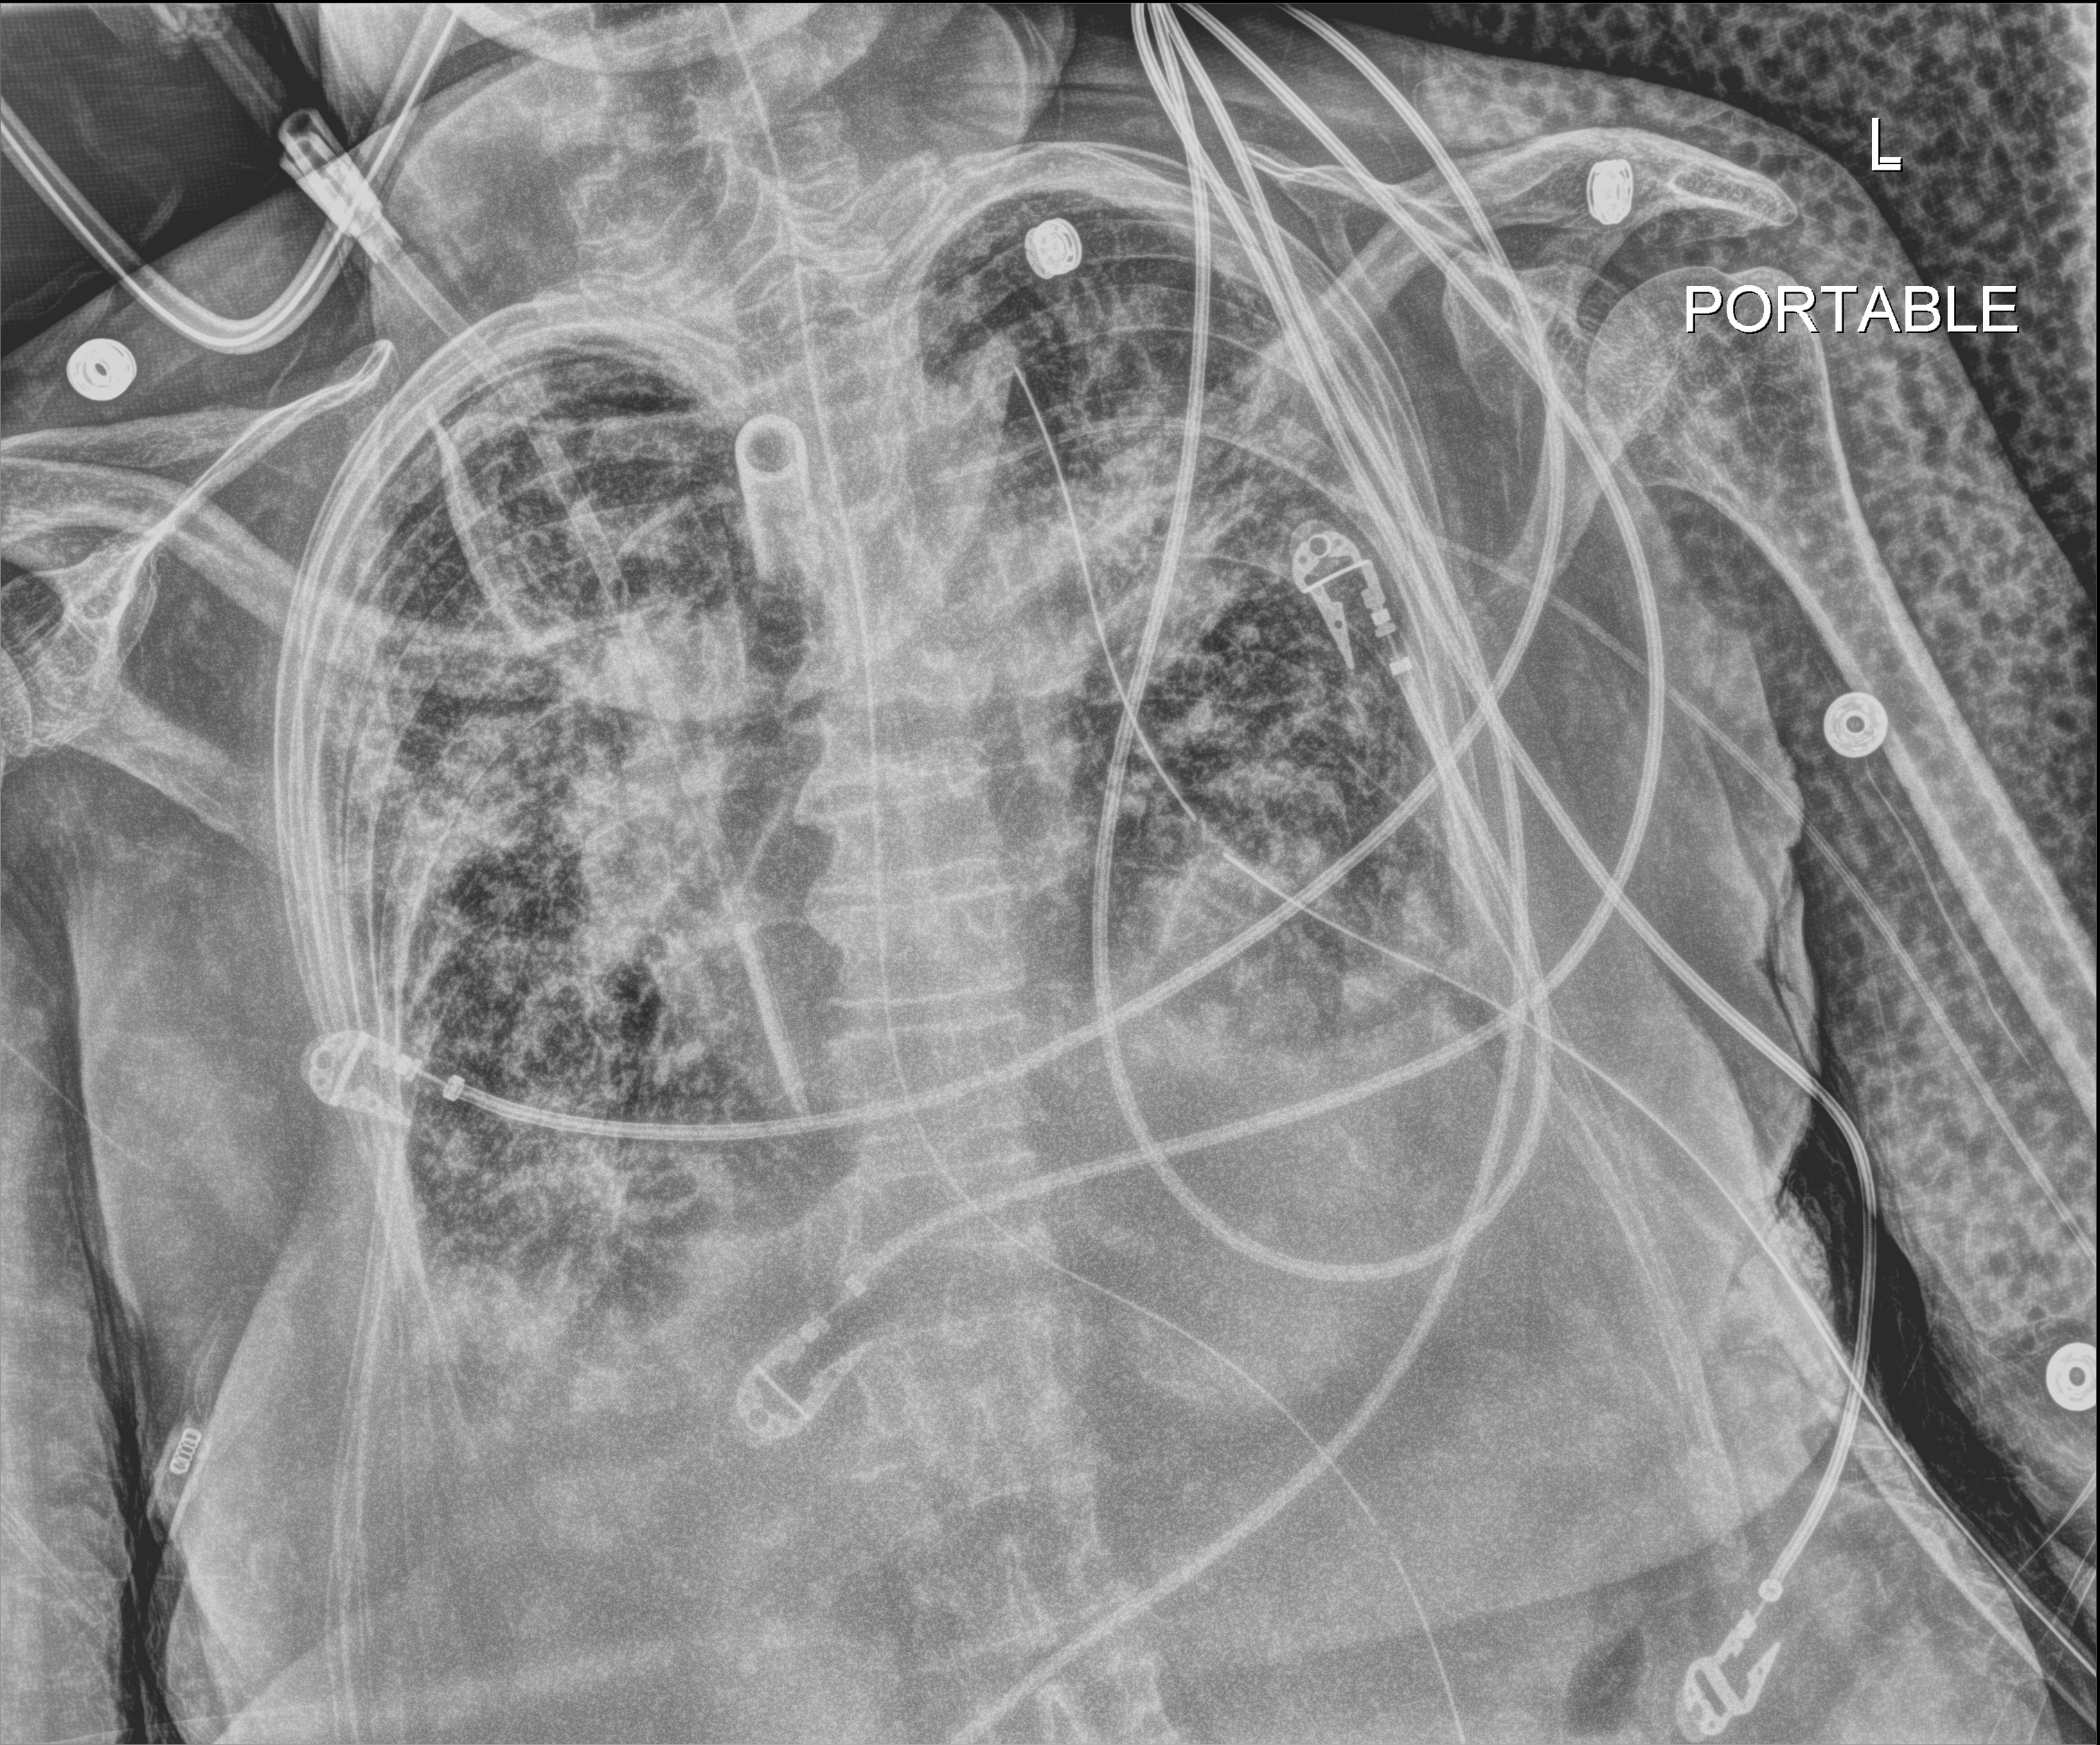
Chest radiograph, anteroposterior (AP) projection. Female patient hospitalised with COVID-19, age 75–90 years.
From the hospital-stay record, not from the radiograph (when in the stay this image was taken is not recorded):
- mechanically ventilated during this hospital stay: yes